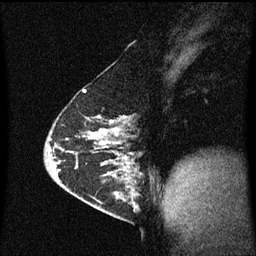
Breast MRI (dynamic contrast-enhanced), one sagittal slice; position 34 of 60 along the scan axis; dynamic contrast-enhanced series, image 2 of 3 at this slice position (ordered by acquisition); 1.5 T; TE 4.2 ms, TR 8.4 ms; 2 mm slice thickness; 256 × 256 image matrix, field of view 200 × 200 mm. Female patient, age 63 years.
Outlined on this slice (semi-automatically segmented with operator editing):
- analysis volume of interest (the breast-tissue region the enhancement analysis was run in; not a lesion): box from (x=98, y=168) to (x=143, y=217) px
- tumour enhancement mask (voxels above the 70 % enhancement threshold inside the analysis volume of interest): (x=104, y=168)–(x=143, y=209)